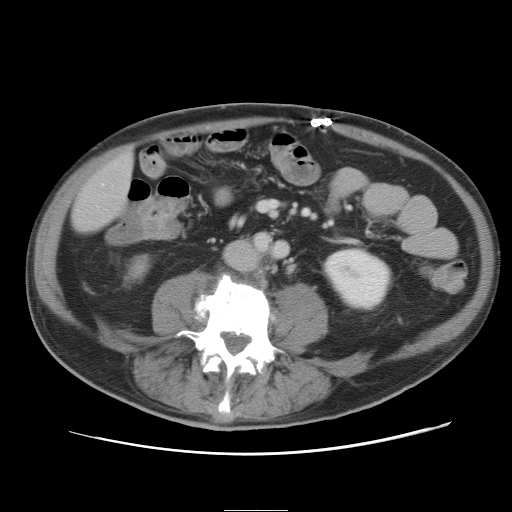
Contrast-enhanced abdominal CT, one axial slice; slice 3 of 89 in the series (ordered by position); soft-tissue window (W 400 / L 40 HU); 5 mm slice thickness; 512 × 512 image matrix, field of view 375 × 375 mm. Male patient, age 69 years. From the clinical record (not read from this slice): diagnosis: colorectal cancer liver metastases, imaged before liver resection.
Annotated regions visible in this slice (outlined manually by an expert reader):
- liver: bounding box [x1, y1, x2, y2] px = [73, 155, 133, 233]
- planned liver remnant (the part of the liver to remain after resection): [73, 155, 133, 233]